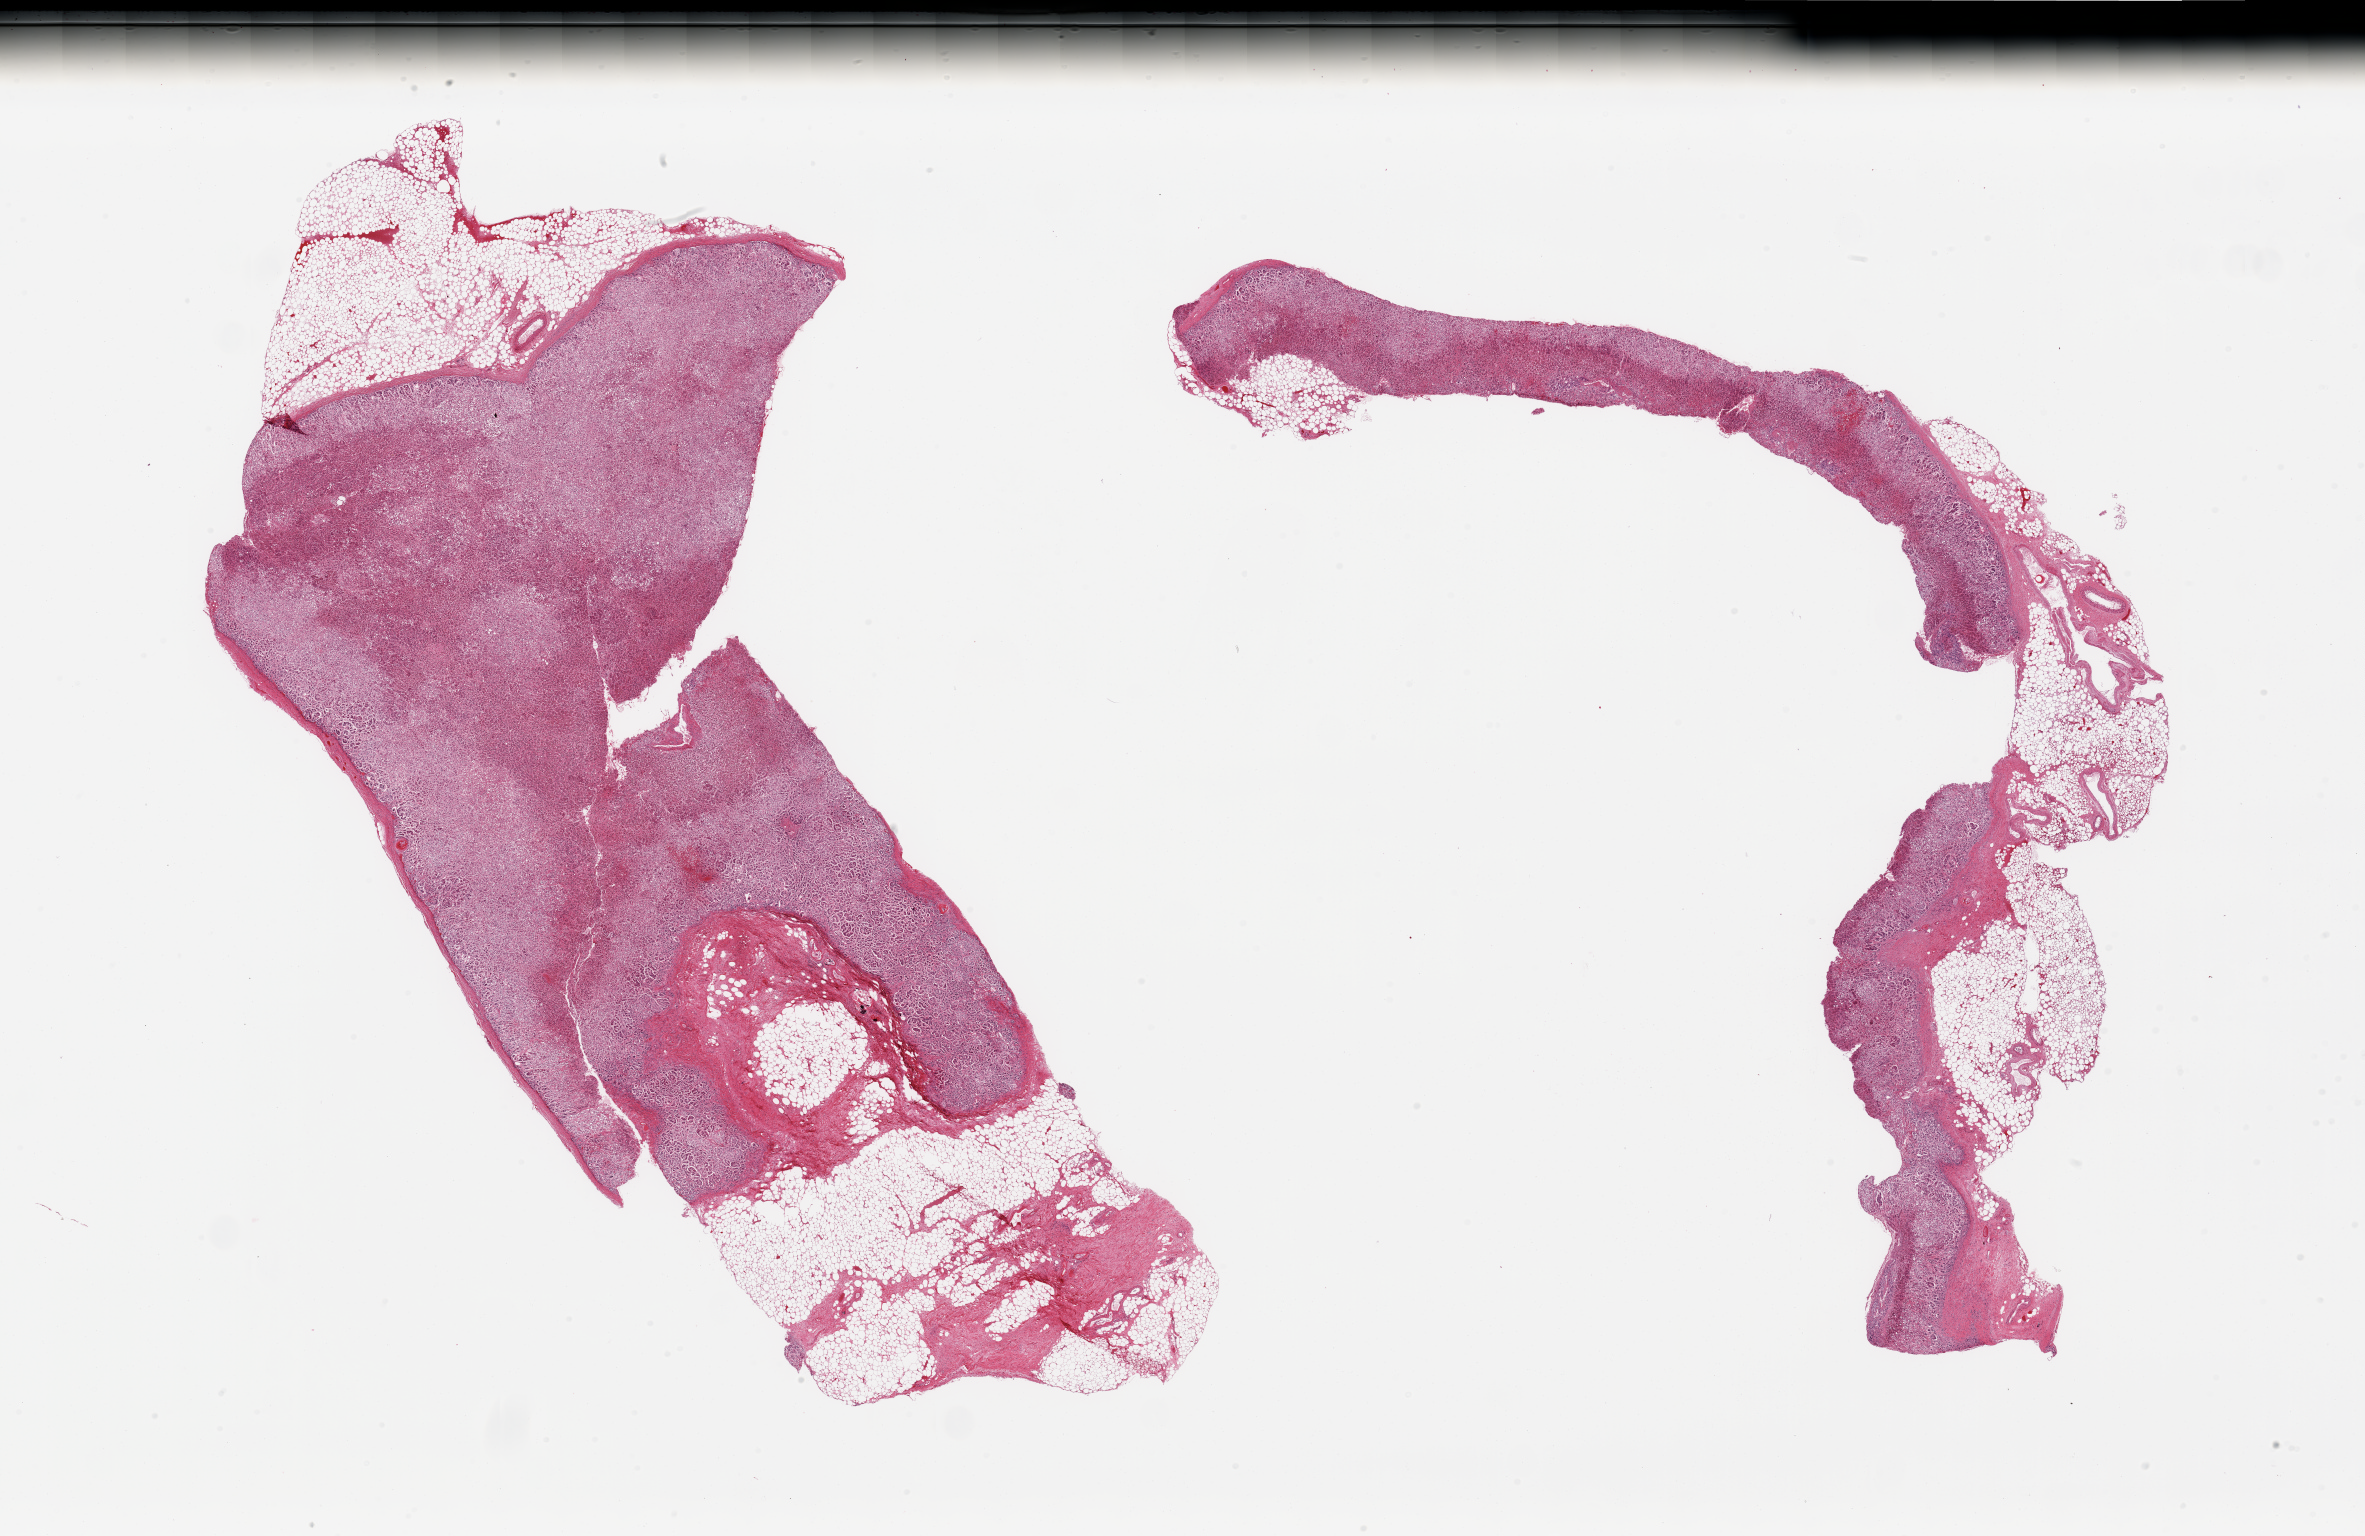
Digitized haematoxylin and eosin-stained section — low-resolution overview of the scanned area, about 37.4 x 24.3 mm; PAXgene-fixed, paraffin-embedded tissue; target tissue: adrenal gland; donor tissue sample.
Review note (as recorded): 2 pieces; moderately to severely autolyzed adrenal cortex; ~30% external fat.